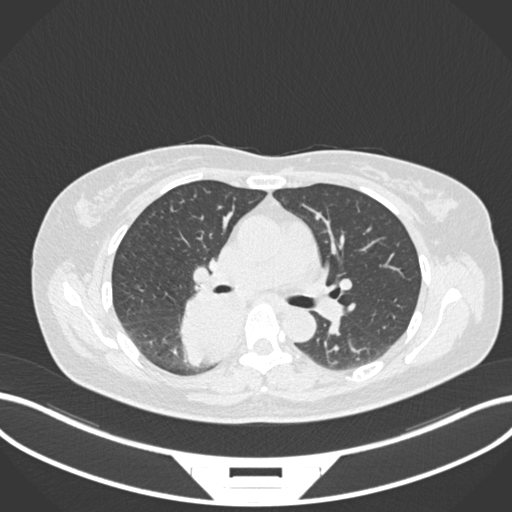
Chest CT, one axial slice. Position 608 of 677 along the scan axis. 120 kVp. Lung window (W 1500 / L -600 HU). 512 × 512 image matrix, field of view 400 × 400 mm. Patient: female, 54 years. Case-level facts recorded for this patient, not image findings: clinical TNM (as recorded): T4 N0 M0.
Structures marked on this image (rectangle marked by the reading radiologist):
- lung tumour (recorded histology: adenocarcinoma): bounding box (x1, y1, x2, y2) in pixels: (179, 290, 243, 373)